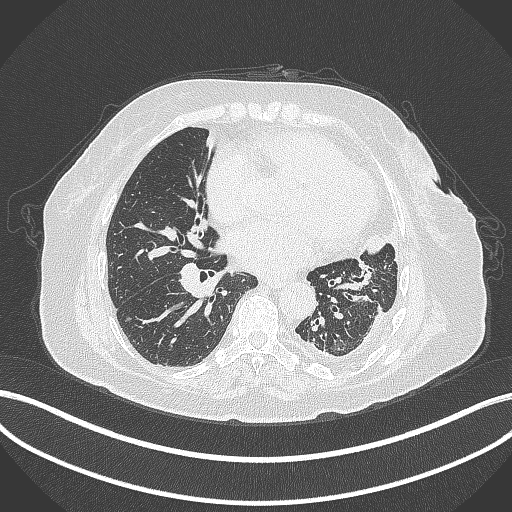
Chest CT, one axial slice. Position 162 of 399 along the scan axis. Reconstruction kernel B70f. Lung window (W 1500 / L -600 HU). 1 mm slice thickness. 512 × 512 image matrix, field of view 400 × 400 mm. Patient: female, 75 years. Case-level facts recorded for this patient, not image findings: clinical TNM (as recorded): T3 N3 M1.
Structures marked on this image (rectangle marked by the reading radiologist):
- lung tumour (recorded histology: adenocarcinoma): bounding box [x1, y1, x2, y2] px = [361, 225, 399, 260]